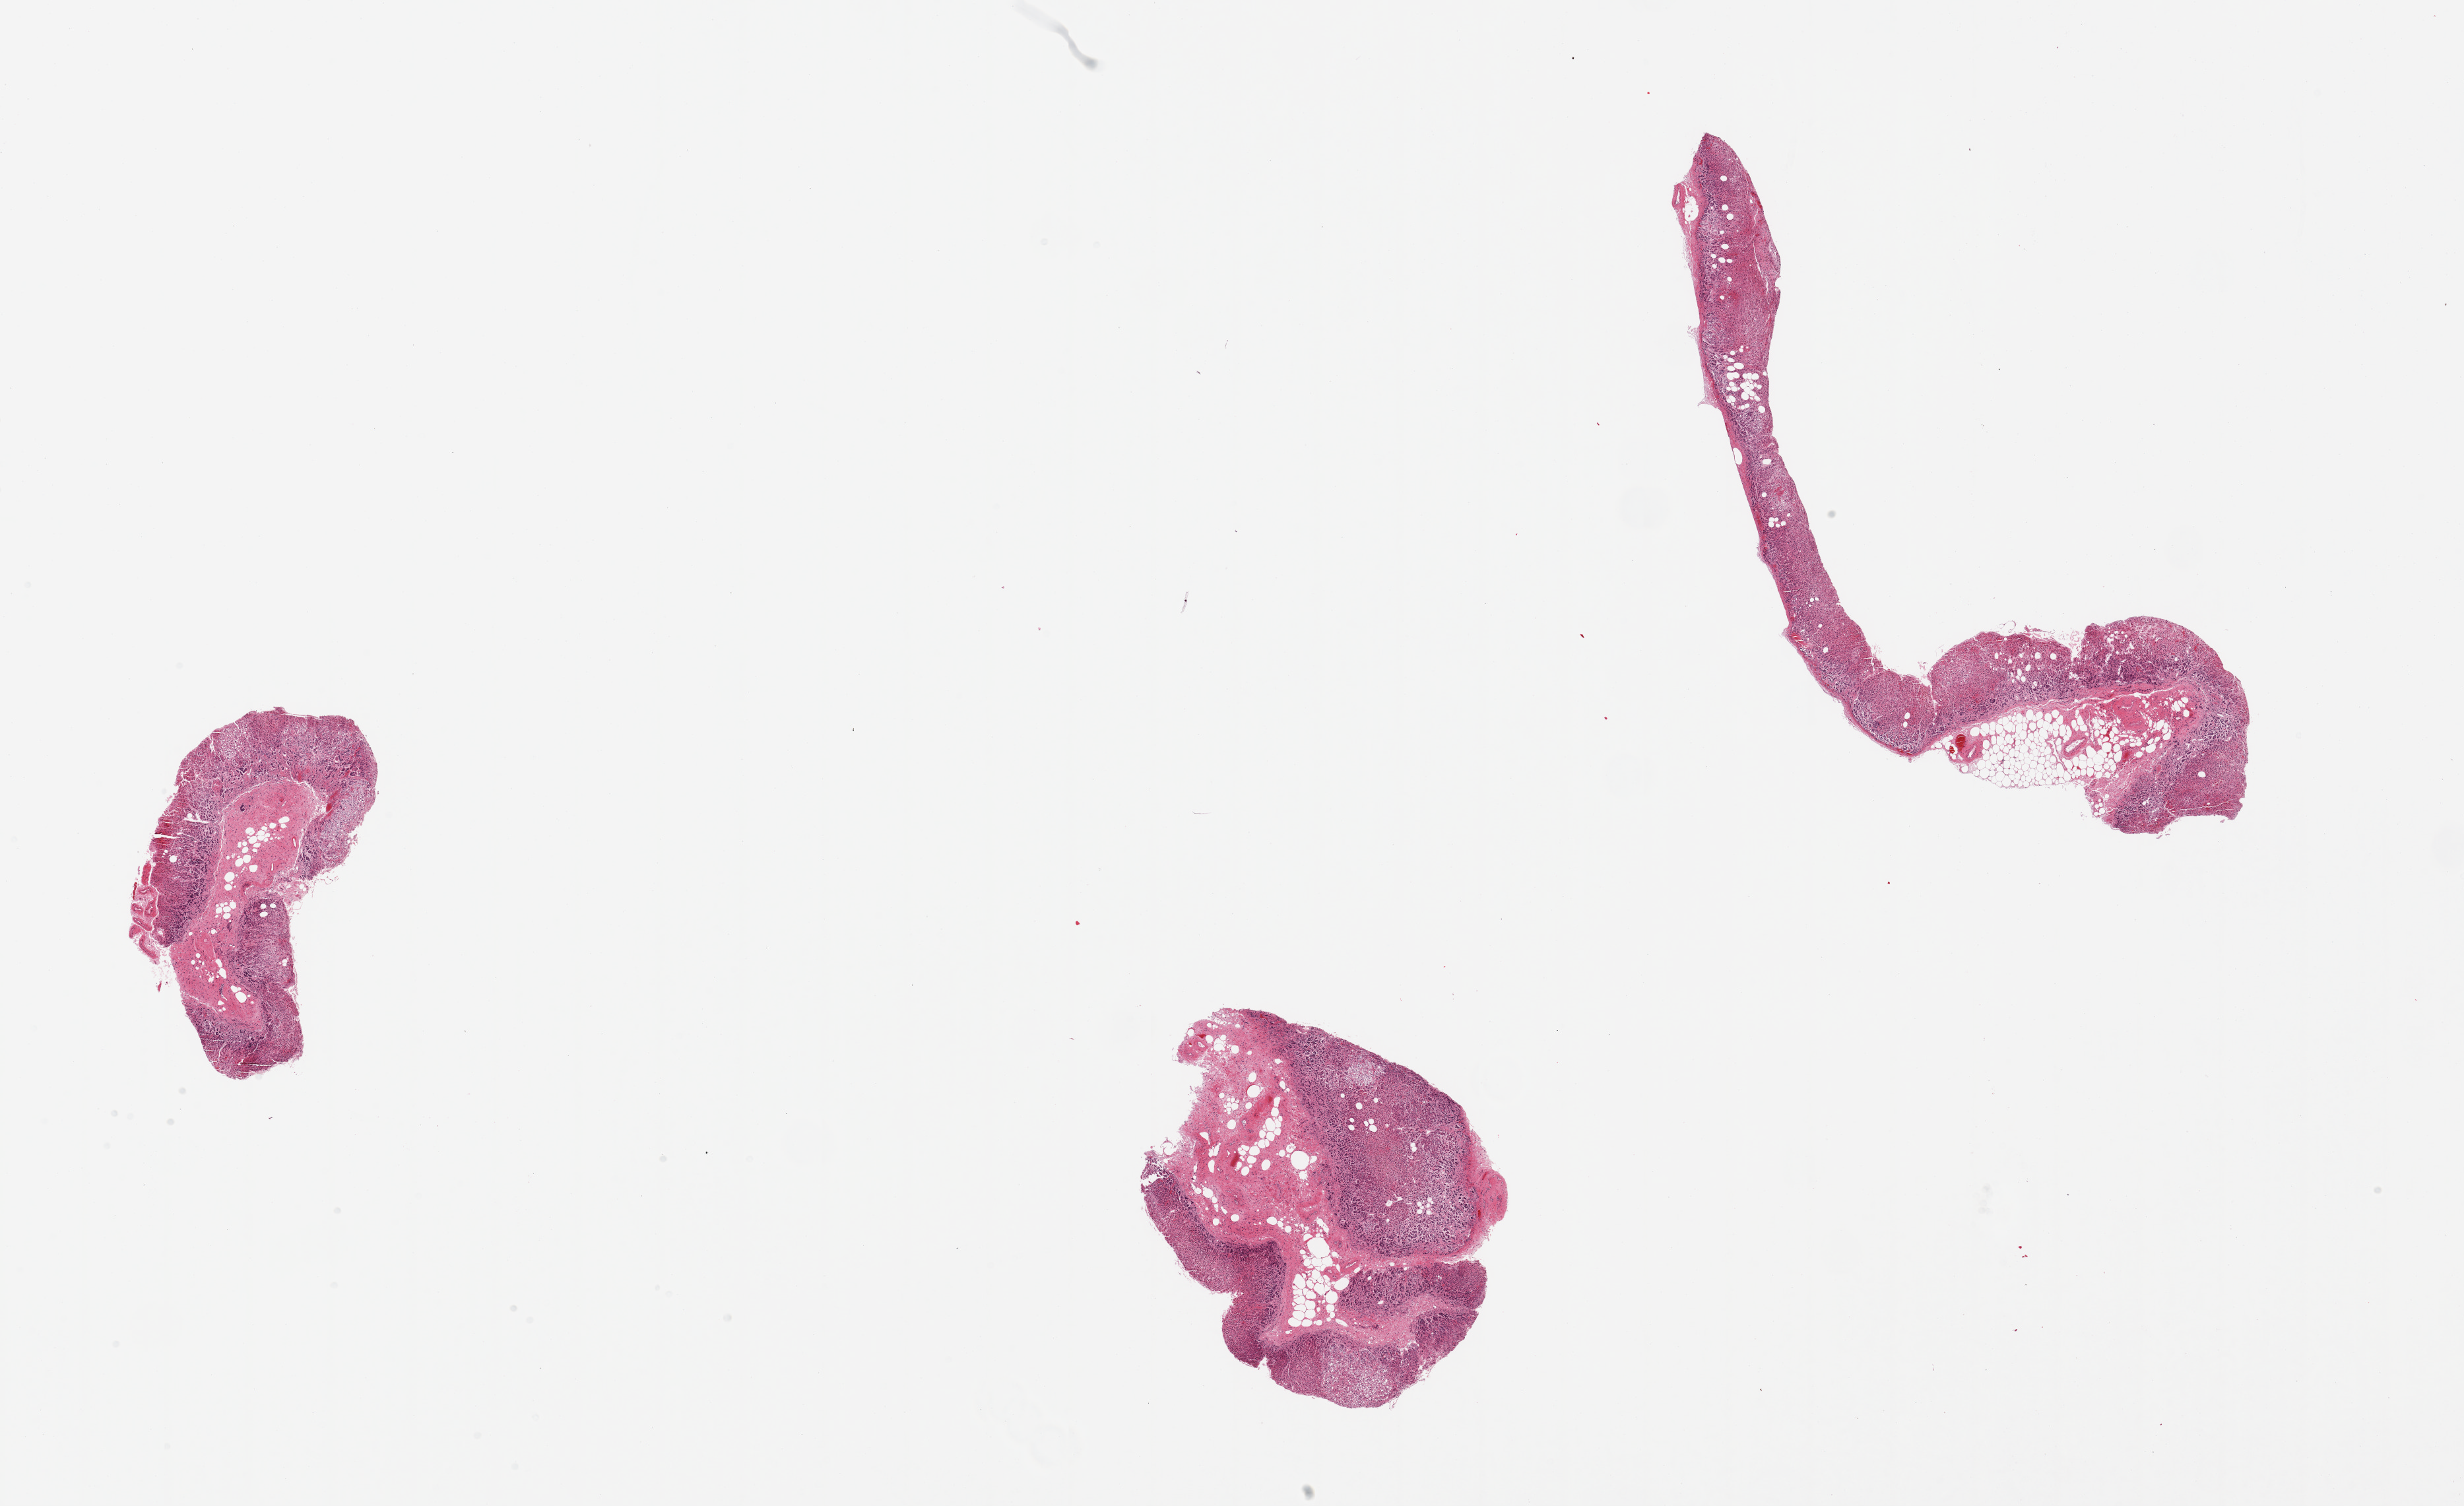
Whole-slide image, hematoxylin and eosin (H&E) stain, brightfield, whole scanned area (about 29.5 x 18.0 mm) shown as a low-resolution overview. PAXgene-fixed, paraffin-embedded tissue. Section of adrenal gland (target tissue). Tissue donor sample. Donor sex: male.
Review note (as recorded): 3 small pieces; 30% fat.